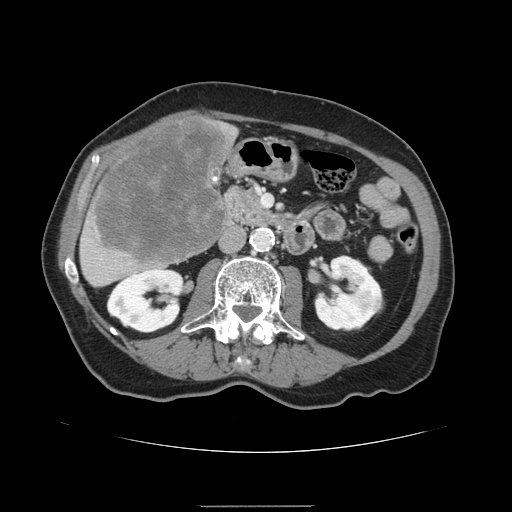
Contrast-enhanced abdominal CT, one axial slice. Position 53 of 168 along the scan axis. Intravenous contrast given. Soft-tissue window (W 400 / L 40 HU). 2.5 mm slice thickness. 512 × 512 image matrix, field of view 386 × 386 mm. Male patient, age 74 years. Case-level facts recorded for this patient, not image findings: diagnosis: colorectal cancer liver metastases, imaged before liver resection; multiple liver metastases: no.
Annotated regions visible in this slice (manually delineated by an expert):
- liver: box from (x=79, y=115) to (x=238, y=287) px
- liver metastasis: (x=91, y=119)–(x=230, y=266)